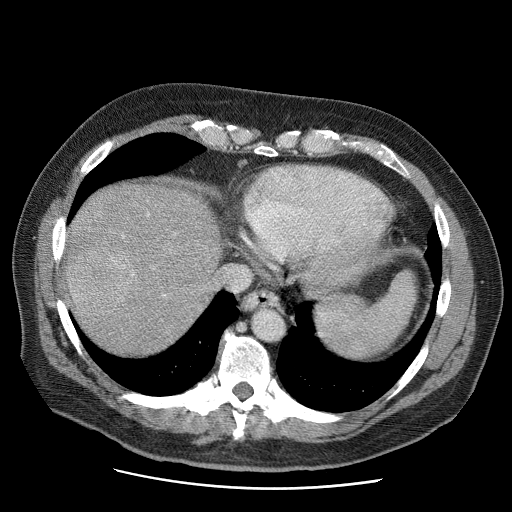
Contrast-enhanced abdominal CT (liver protocol), one axial slice; position 54 of 81 along the scan axis; reconstruction kernel STANDARD; 120 kVp; soft-tissue window (W 400 / L 40 HU); 2.5 mm slice thickness; 512 × 512 image matrix, field of view 380 × 380 mm. Case-level facts recorded for this patient, not image findings: diagnosis: hepatocellular carcinoma (patient treated with transarterial chemoembolisation; whether this scan precedes or follows treatment is not stated here); TNM stage (as recorded): Stage-IIIA.
Structures marked on this image (semi-automatic segmentation, software-assisted and operator-edited):
- liver parenchyma outside the tumour (the mass and vessels are separate outlines, so this box may not span the whole liver): bounding box [x1, y1, x2, y2] px = [64, 182, 220, 354]
- mass: [67, 235, 137, 316]